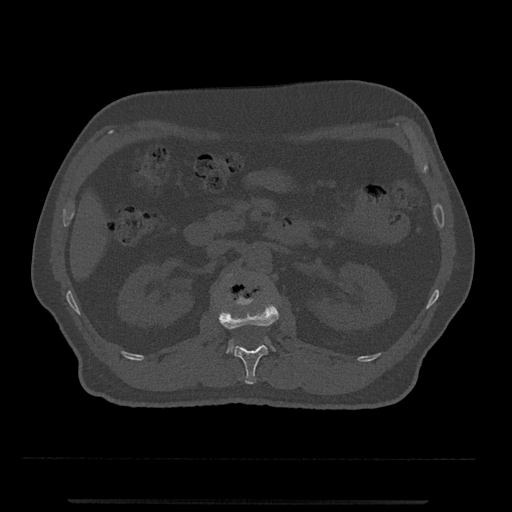
CT including the spine, one axial slice; position 310 of 797 along the scan axis; bone window (W 1800 / L 400 HU); 0.5 mm slice thickness; 512 × 512 image matrix, field of view 419 × 419 mm. Patient: male, 63 years. Case-level facts recorded for this patient, not image findings: primary cancer: prostate.
Annotated regions visible in this slice (semi-automatically segmented with operator editing):
- L1 vertebra: bounding box [x1, y1, x2, y2] px = [218, 296, 279, 384]
- L2 vertebra: [226, 274, 274, 353]